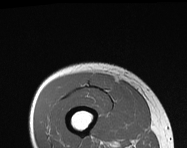
MRI of an extremity soft-tissue mass, one axial slice; slice 33 of 114 in the series (ordered by position); MR volume resampled by the dataset authors to the PET/CT grid (not the native acquisition matrix); 3.27 mm slice thickness; 187 × 148 image matrix, field of view 183 × 145 mm. Male patient. Case-level facts recorded for this patient, not image findings: histological type: pleiomorphic leiomyosarcoma; grade: intermediate; site of the primary tumour: right thigh.
Outlined on this slice (expert contour drawn on MRI and transferred to this co-registered scan by the dataset authors):
- gross tumour volume including surrounding oedema: bounding box (x1, y1, x2, y2) in pixels: (89, 72, 113, 91)